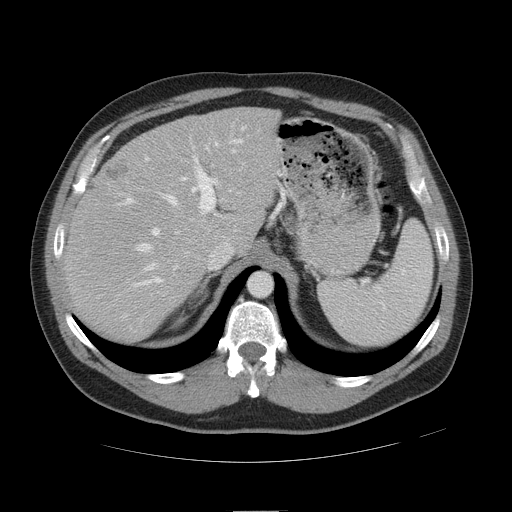
Contrast-enhanced abdominal CT, one axial slice; slice 33 of 49 in the series (ordered by position); 120 kVp; intravenous contrast given; soft-tissue window (W 400 / L 40 HU); 5 mm slice thickness; 512 × 512 image matrix, field of view 425 × 425 mm. Male patient, age 52 years. From the clinical record (not read from this slice): diagnosis: colorectal cancer liver metastases, imaged before liver resection; multiple liver metastases: yes; largest metastasis: 5.1 cm.
Structures marked on this image (manually delineated by an expert):
- hepatic veins: bounding box [x1, y1, x2, y2] px = [136, 145, 237, 271]
- liver: [66, 109, 275, 338]
- planned liver remnant (the part of the liver to remain after resection): [135, 109, 275, 247]
- portal vein (with intrahepatic branches): [117, 126, 246, 288]
- liver metastasis: [106, 167, 127, 178]